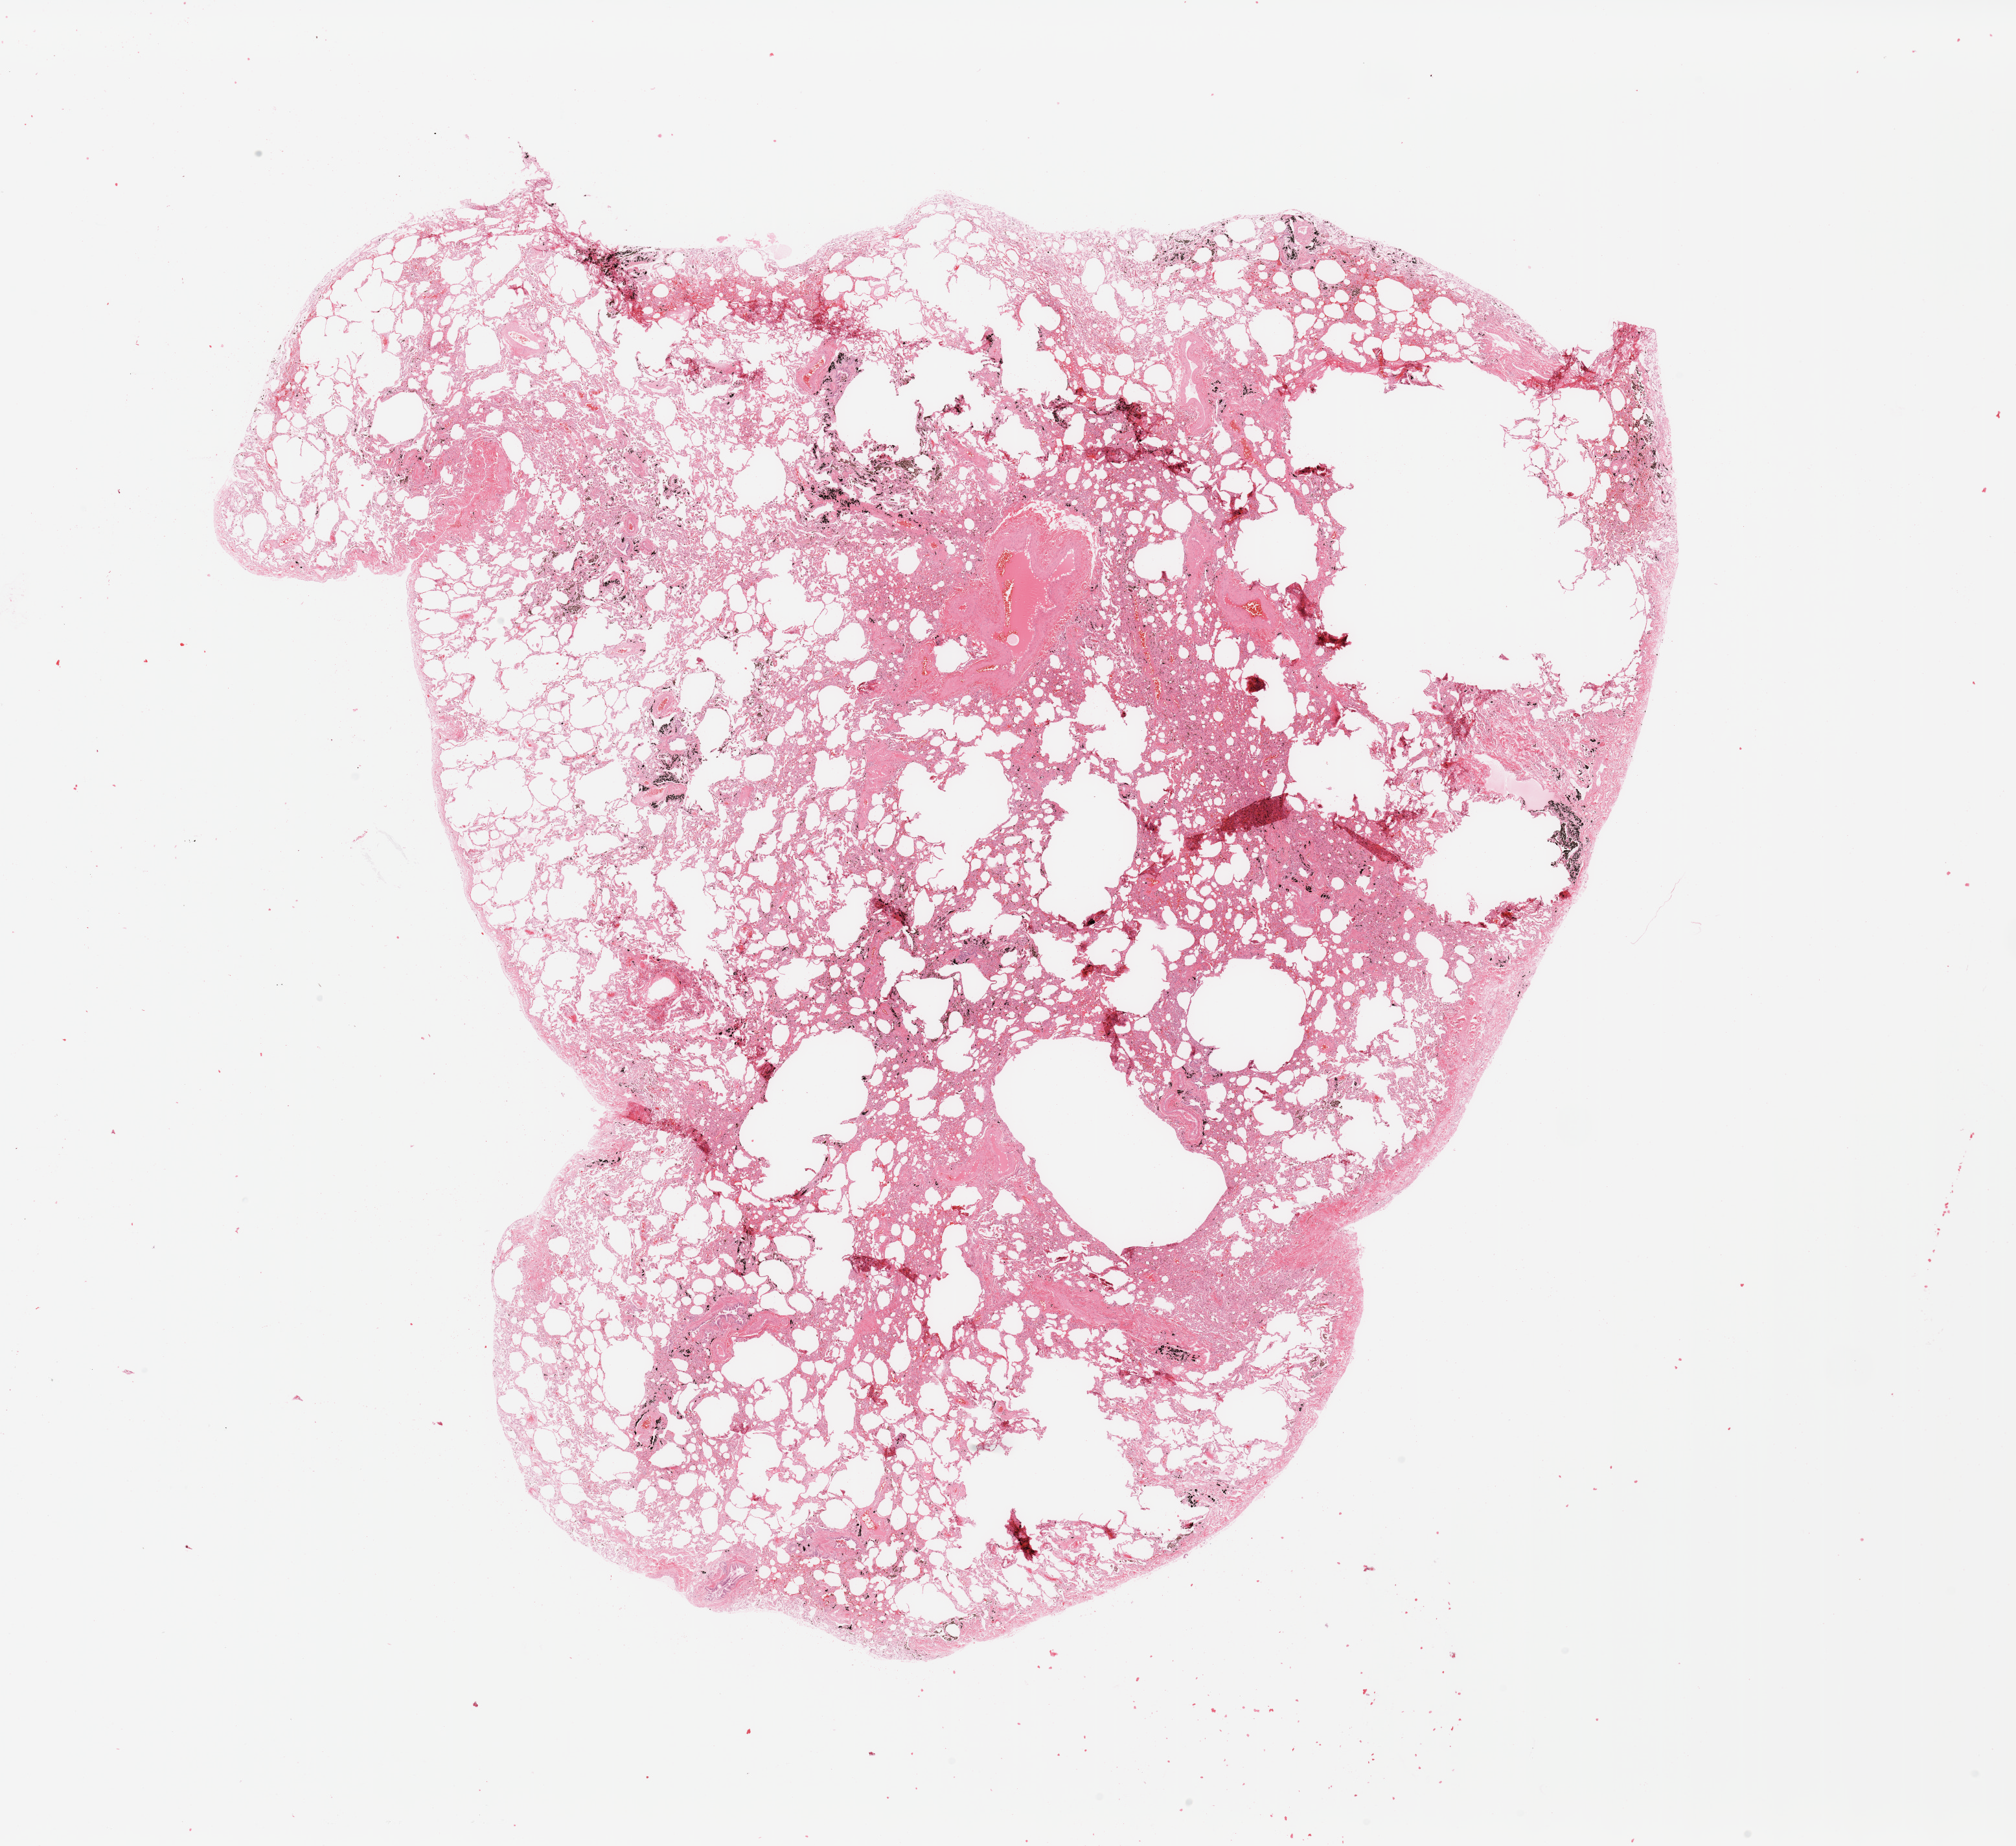
Whole-slide histology image, H&E, shown as a low-resolution overview of the whole scanned area (about 24.6 x 22.5 mm). Normal (non-tumour) tissue sample, lung. Patient: male, age 52 years.
• this section: normal (non-tumour) tissue from the same patient
• patient diagnosis: Squamous cell carcinoma, NOS